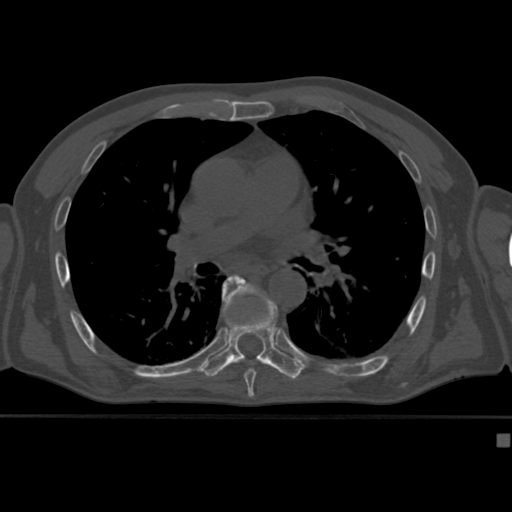
CT including the spine, one axial slice. Slice 270 of 430 in the series (ordered by position). Reconstruction kernel Br40s. 120 kVp. Bone window (W 1800 / L 400 HU). 512 × 512 image matrix, field of view 337 × 337 mm. Patient: male, 64 years. Case-level facts recorded for this patient, not image findings: primary cancer: uterus.
Outlined on this slice (semi-automatic segmentation, software-assisted and operator-edited):
- T7 vertebra: bounding box <223,274,256,382> (left, top, right, bottom; pixels)
- T8 vertebra: <204,276,303,382>